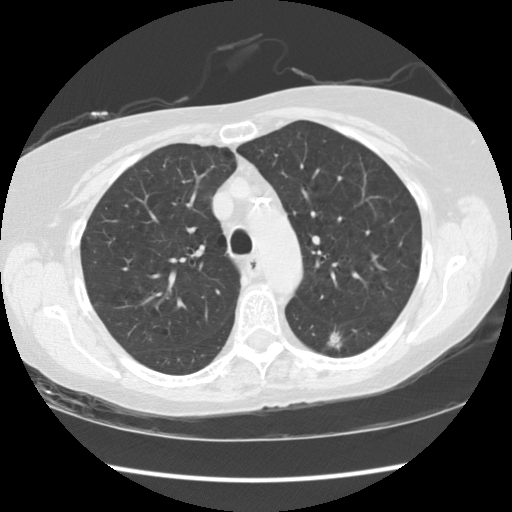
Axial slice from a low-dose chest CT screening exam; third annual screen; lung window (W 1500 / L -600 HU); 2.5 mm slice thickness; standard (soft-tissue) reconstruction kernel (STANDARD). Female participant, aged 63 years at enrolment. Current smoker at enrolment.
• Expert-annotated lung lesion, bounding box [x1, y1, x2, y2] px = [312, 318, 356, 358].
• The screening reader recorded 4 non-calcified nodules or masses ≥4 mm on this exam (left lower lobe, right upper lobe, left upper lobe, left lower lobe); which of them this box marks is not recorded.
• Later outcome: lung cancer diagnosed 60 days after this screen — squamous cell carcinoma, NOS, left lower lobe, moderately differentiated (G2), stage IB (AJCC 6th edition), 15 mm at pathology.